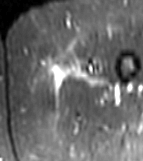
MRI of an extremity soft-tissue mass, one axial slice; slice 6 of 81 in the series (ordered by position); STIR; MR volume resampled by the dataset authors to the PET/CT grid (not the native acquisition matrix); 3.27 mm slice thickness; 143 × 161 image matrix. Female patient. From the clinical record (not read from this slice): histological type: myxofibrosarcoma; grade: intermediate; site of the primary tumour: left thigh.
Structures marked on this image (expert contour drawn on MRI and transferred to this co-registered scan by the dataset authors):
- gross tumour volume including surrounding oedema: bounding box (x1, y1, x2, y2) in pixels: (44, 53, 107, 91)